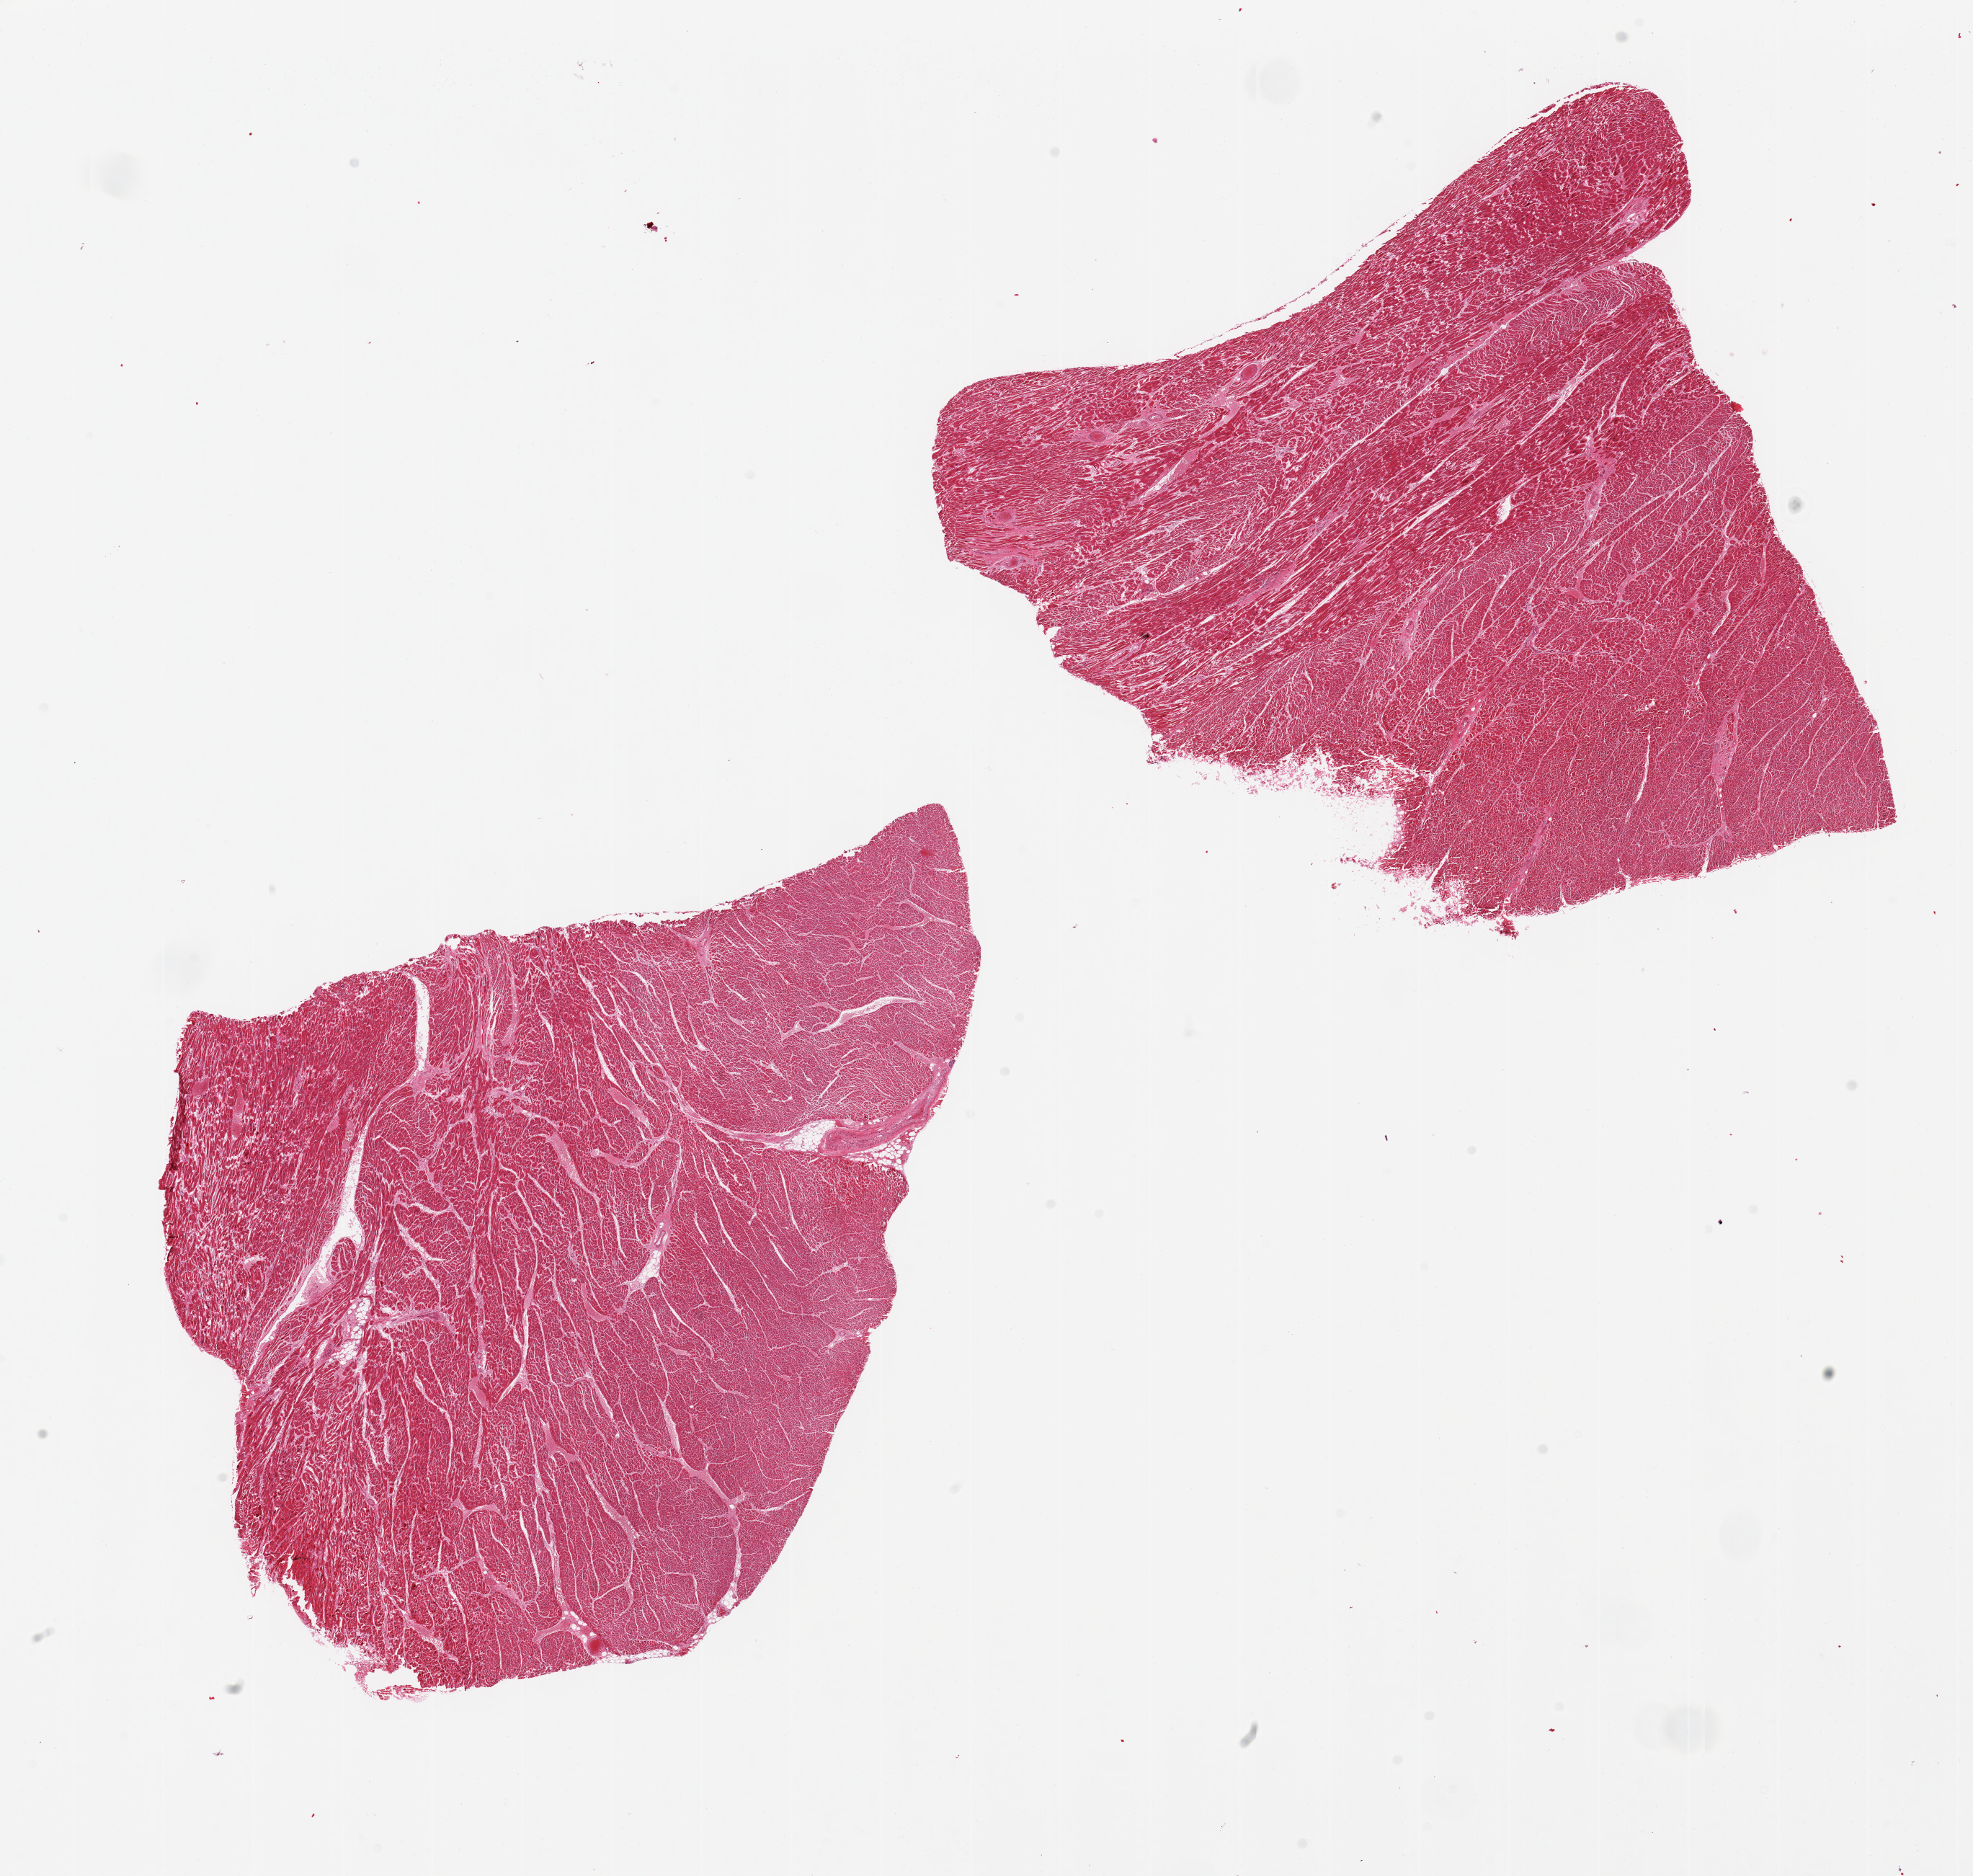
H&E whole-slide image, brightfield — a low-resolution overview of the entire scanned area, about 21.7 x 20.6 mm (slide scanned at 20x), PAXgene-fixed, paraffin-embedded tissue, section of heart (target tissue), donor tissue sample. Donor sex: female.
* reviewer comment on this tissue sample: 2 pieces, patchy interstitial fibrosis